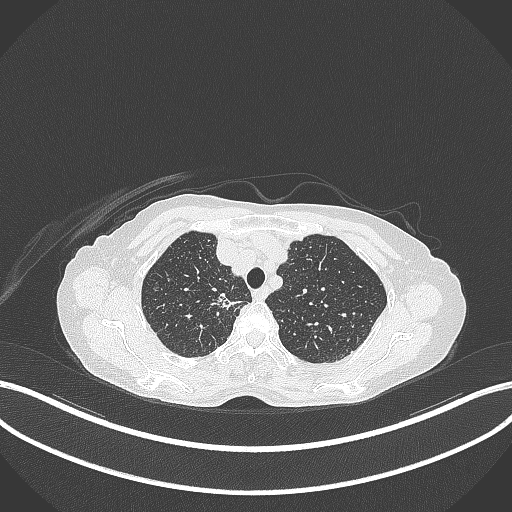
Chest CT, one axial slice; 120 kVp; lung window (W 1500 / L -600 HU); 1 mm slice thickness; 512 × 512 image matrix, field of view 400 × 400 mm. Female patient, age 75 years. Case-level facts recorded for this patient, not image findings: clinical TNM (as recorded): T1c N1 M1.
Outlined on this slice (rectangle marked by the reading radiologist):
- lung tumour (recorded histology: adenocarcinoma): bounding box <213,291,247,313> (left, top, right, bottom; pixels)